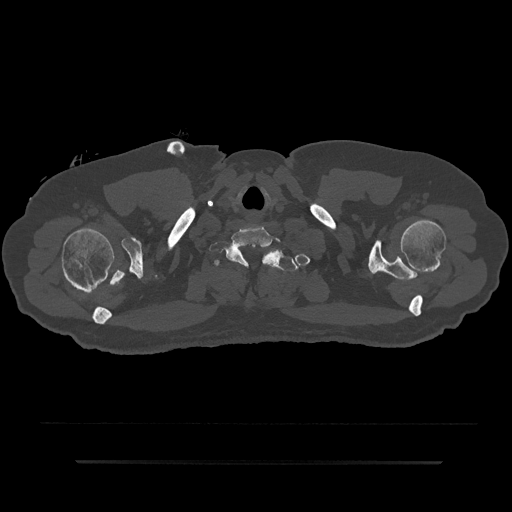
CT including the spine, one axial slice; position 760 of 797 along the scan axis; 120 kVp; bone window (W 1800 / L 400 HU); 512 × 512 image matrix, field of view 464 × 464 mm. Patient: male, 59 years. Case-level facts recorded for this patient, not image findings: primary cancer: bile ducts; vertebrae with lytic lesions (as recorded): T10.
Outlined on this slice (semi-automatically segmented with operator editing):
- T1 vertebra: bounding box <213,252,301,271> (left, top, right, bottom; pixels)